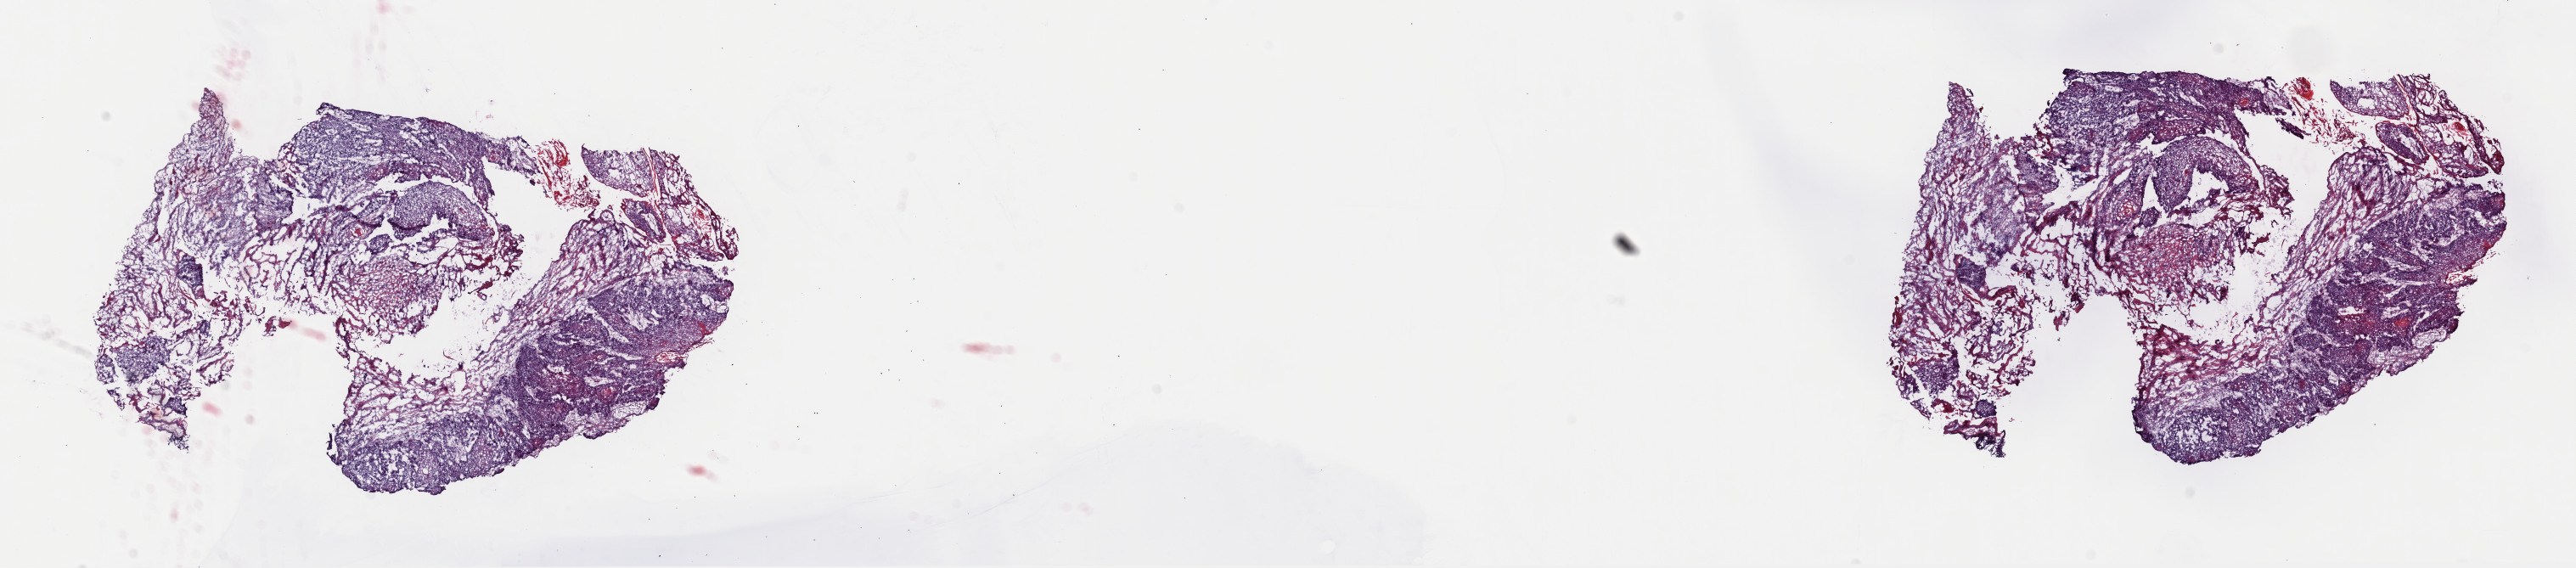
Digitized H&E-stained tissue section (whole slide) — whole scanned area (about 24.0 x 5.3 mm, from a 40x scan) shown as a low-resolution overview; frozen section from the top of the tissue portion; primary tumour sample from the head and neck. Patient: male, age at initial diagnosis 59 years. Histologic grade: G2 (moderately differentiated). Pathologist review of this section (percent, as recorded): tumour cells 50%, tumour nuclei 100%, normal cells 0%, stromal cells 50%, necrosis 0%. Inflammatory infiltration, as recorded: lymphocyte infiltration 2%, monocyte infiltration 1%, neutrophil infiltration 0%.
- pathologic diagnosis: Squamous cell carcinoma, keratinizing, NOS